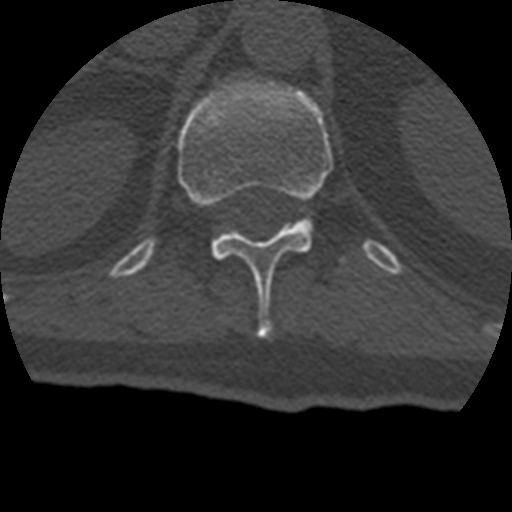
CT including the spine, one axial slice. Position 168 of 399 along the scan axis. Reconstruction kernel STANDARD. Bone window (W 1800 / L 400 HU). 1.25 mm slice thickness. 512 × 512 image matrix, field of view 160 × 160 mm. Patient age 69 years. From the clinical record (not read from this slice): primary cancer: prostate.
Structures marked on this image (semi-automatic segmentation, software-assisted and operator-edited):
- T12 vertebra: box from (x=178, y=79) to (x=333, y=338) px